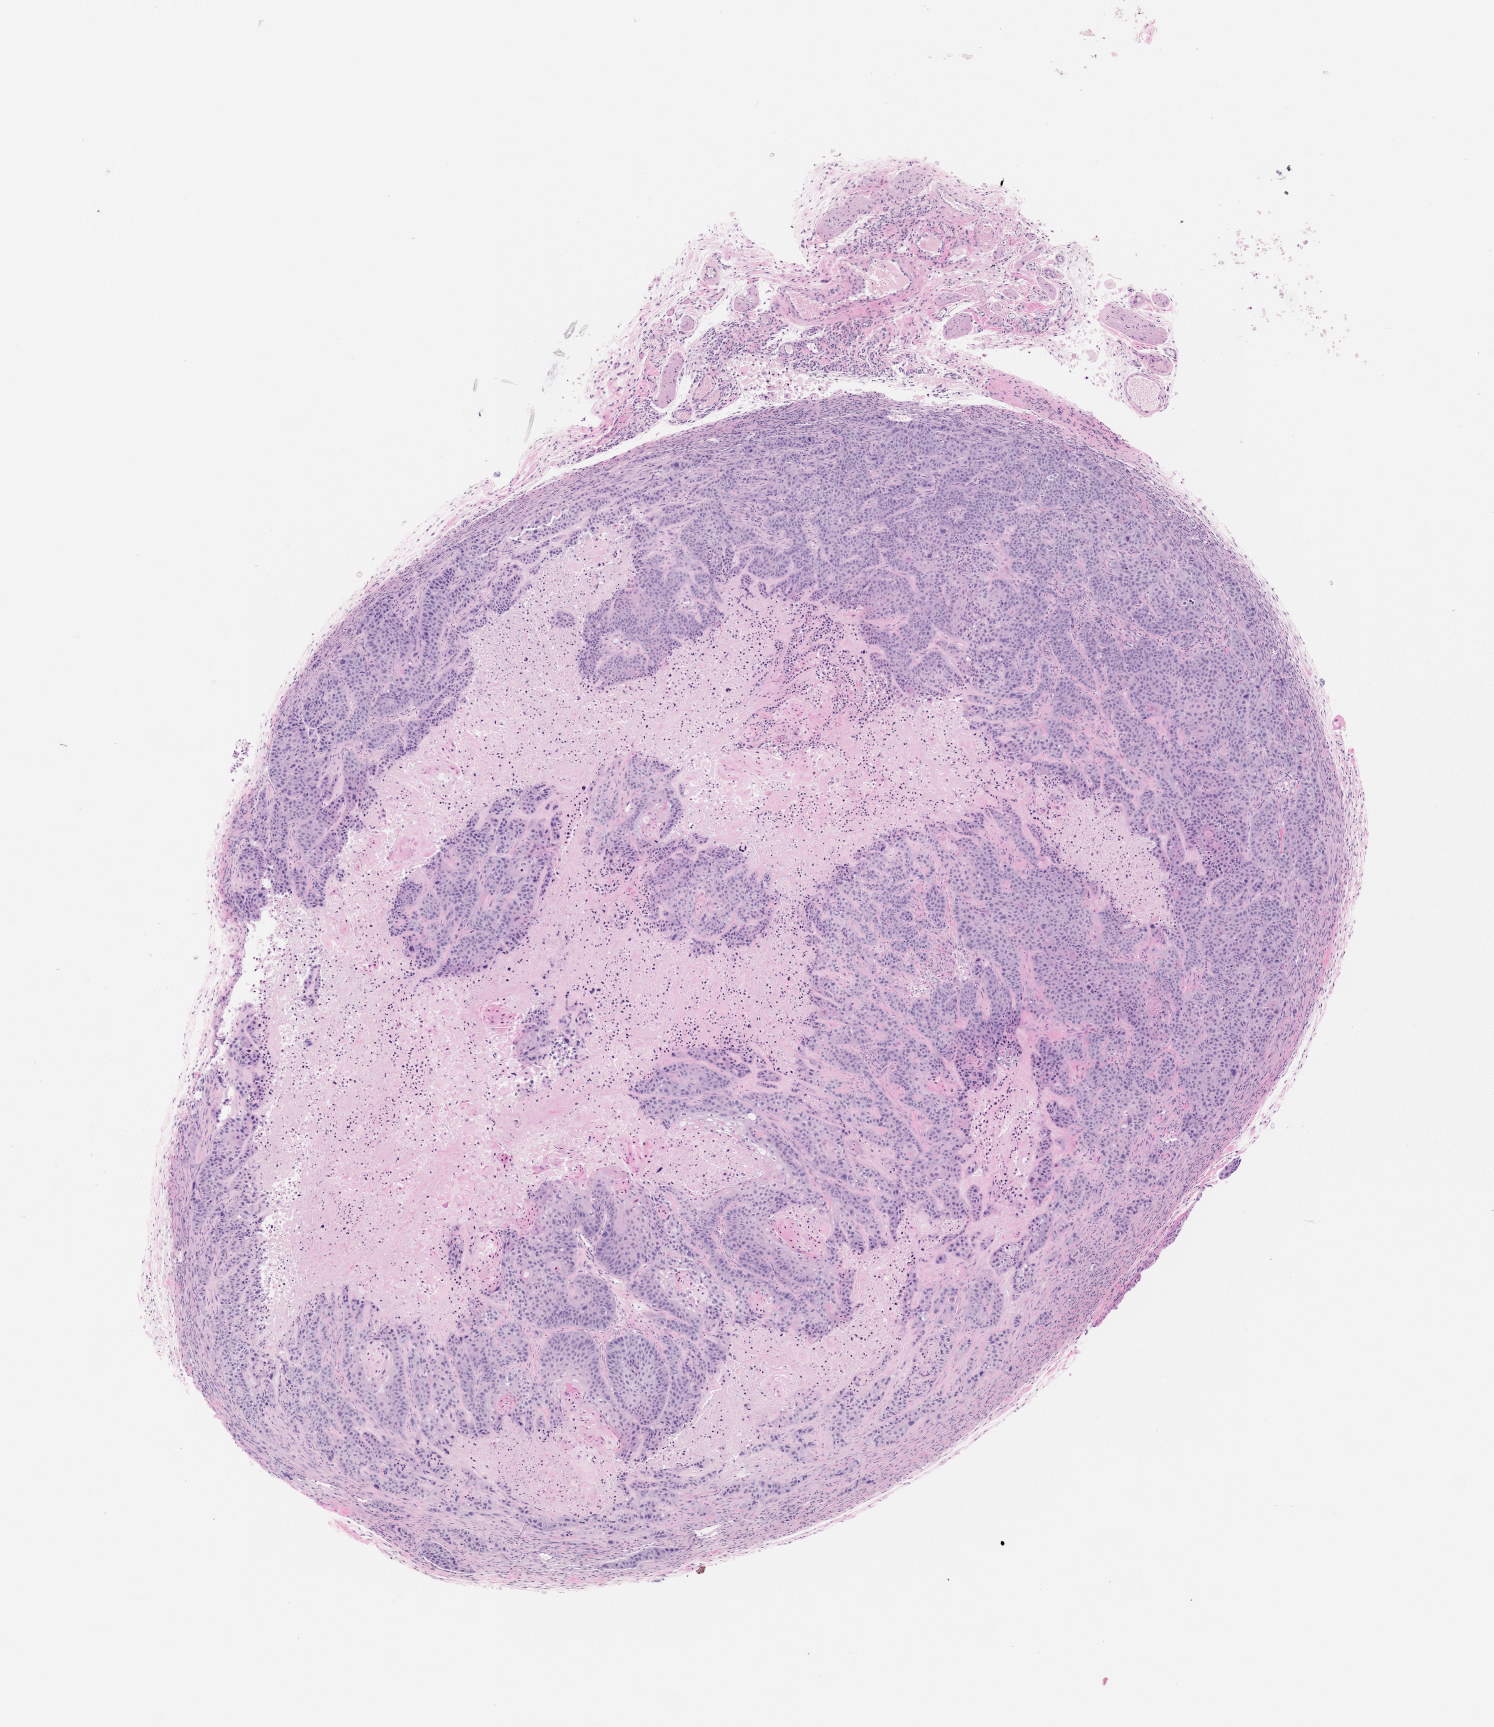
Whole-slide image, hematoxylin and eosin (H&E): patient-derived xenograft (human tumor grown in a mouse), passage 2 — whole scanned area (about 6.0 x 6.9 mm) shown as a low-resolution overview; formalin-fixed, paraffin-embedded (FFPE) tissue; originating tumor site category: lung.
Originating patient diagnosis: Lung Squamous Cell Carcinoma.